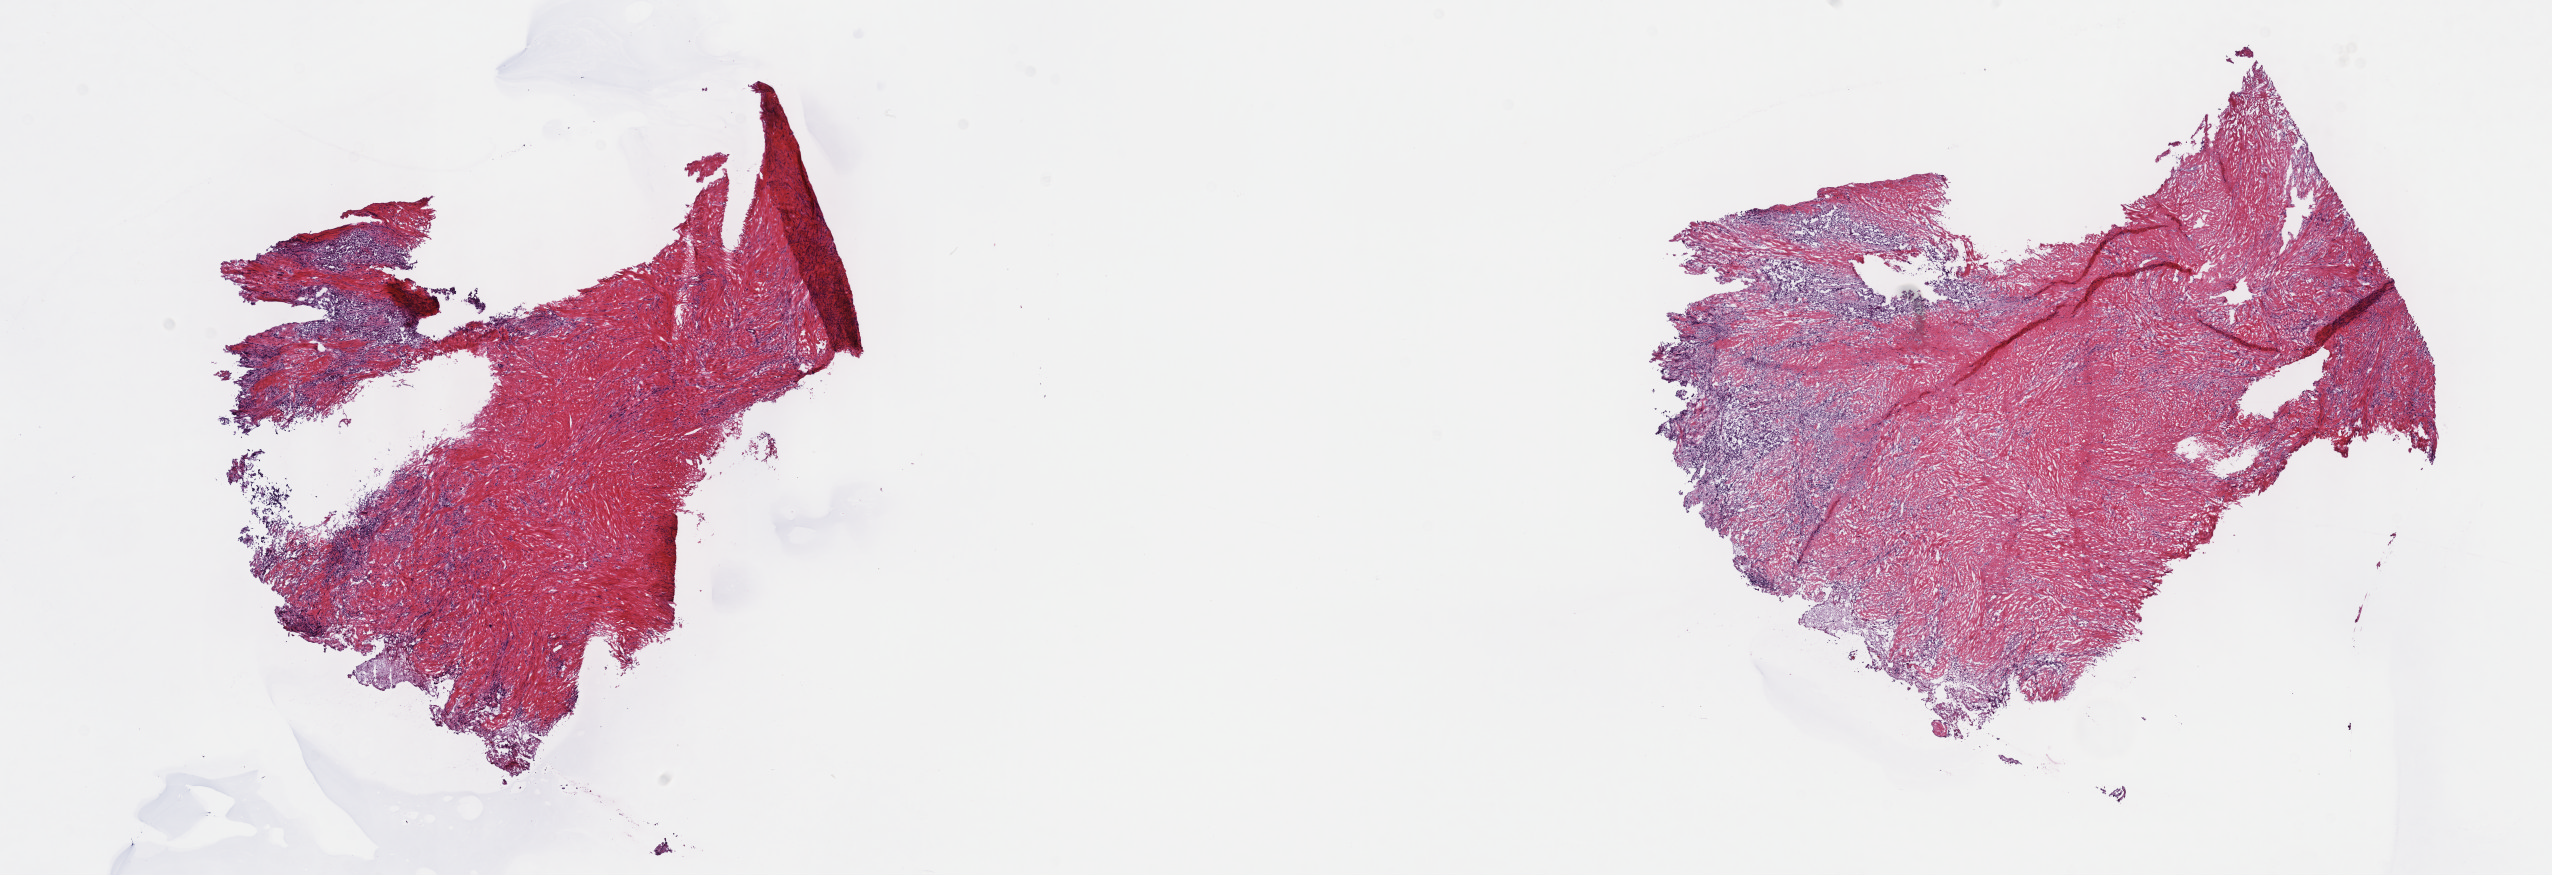
Digitized Hematoxylin and eosin (H&E) stained tissue section (whole slide) — whole scanned area (about 20.6 x 7.1 mm, slide scanned at 40x) shown as a low-resolution overview, frozen section from the top of the tissue portion, primary tumour sample from the mesothelium. Male, age 57 years at initial diagnosis. Slide review estimates, as recorded: tumour cells 65%, tumour nuclei 65%, normal cells 0%, stromal cells 35%, necrosis 0%. Inflammatory infiltration, as recorded: lymphocyte infiltration 3%, monocyte infiltration 1%, neutrophil infiltration 3%.
AJCC pathologic stage: IV (7th edition). Pathologic diagnosis: Epithelioid mesothelioma, malignant (pleura, NOS).